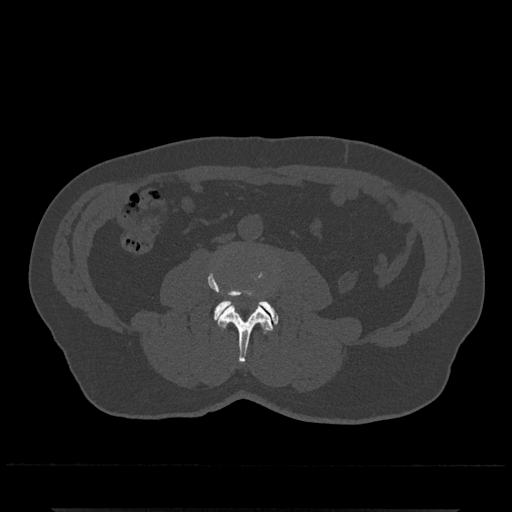
CT including the spine, one axial slice. Position 200 of 797 along the scan axis. Reconstruction kernel Br40s/3. 120 kVp. Bone window (W 1800 / L 400 HU). 0.5 mm slice thickness. 512 × 512 image matrix, field of view 393 × 393 mm. Male patient, age 67 years. From the clinical record (not read from this slice): primary cancer: prostate.
Annotated regions visible in this slice (semi-automatic segmentation, software-assisted and operator-edited):
- L3 vertebra: bounding box (x1, y1, x2, y2) in pixels: (208, 271, 273, 363)
- L4 vertebra: (214, 299, 278, 326)